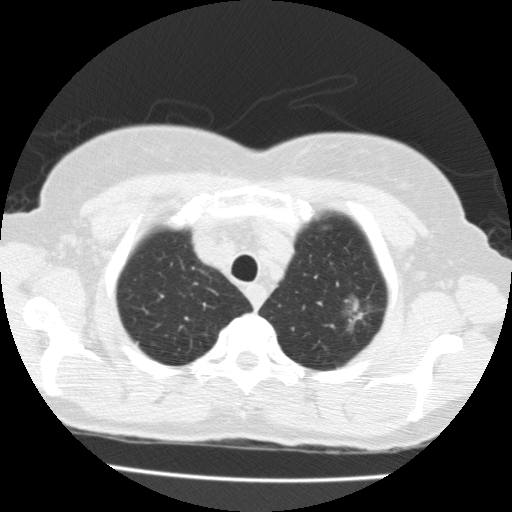
Low-dose screening chest CT, one axial slice; position 157 of 183 along the scan axis; 120 kVp; lung window (W 1500 / L -600 HU); 2 mm slice thickness; 512 × 512 image matrix, field of view 320 × 320 mm.
Outlined on this slice (outlined manually by an expert reader):
- lesion 1 (tumor, upper lobe of left lung): bounding box <344,295,363,324> (left, top, right, bottom; pixels)